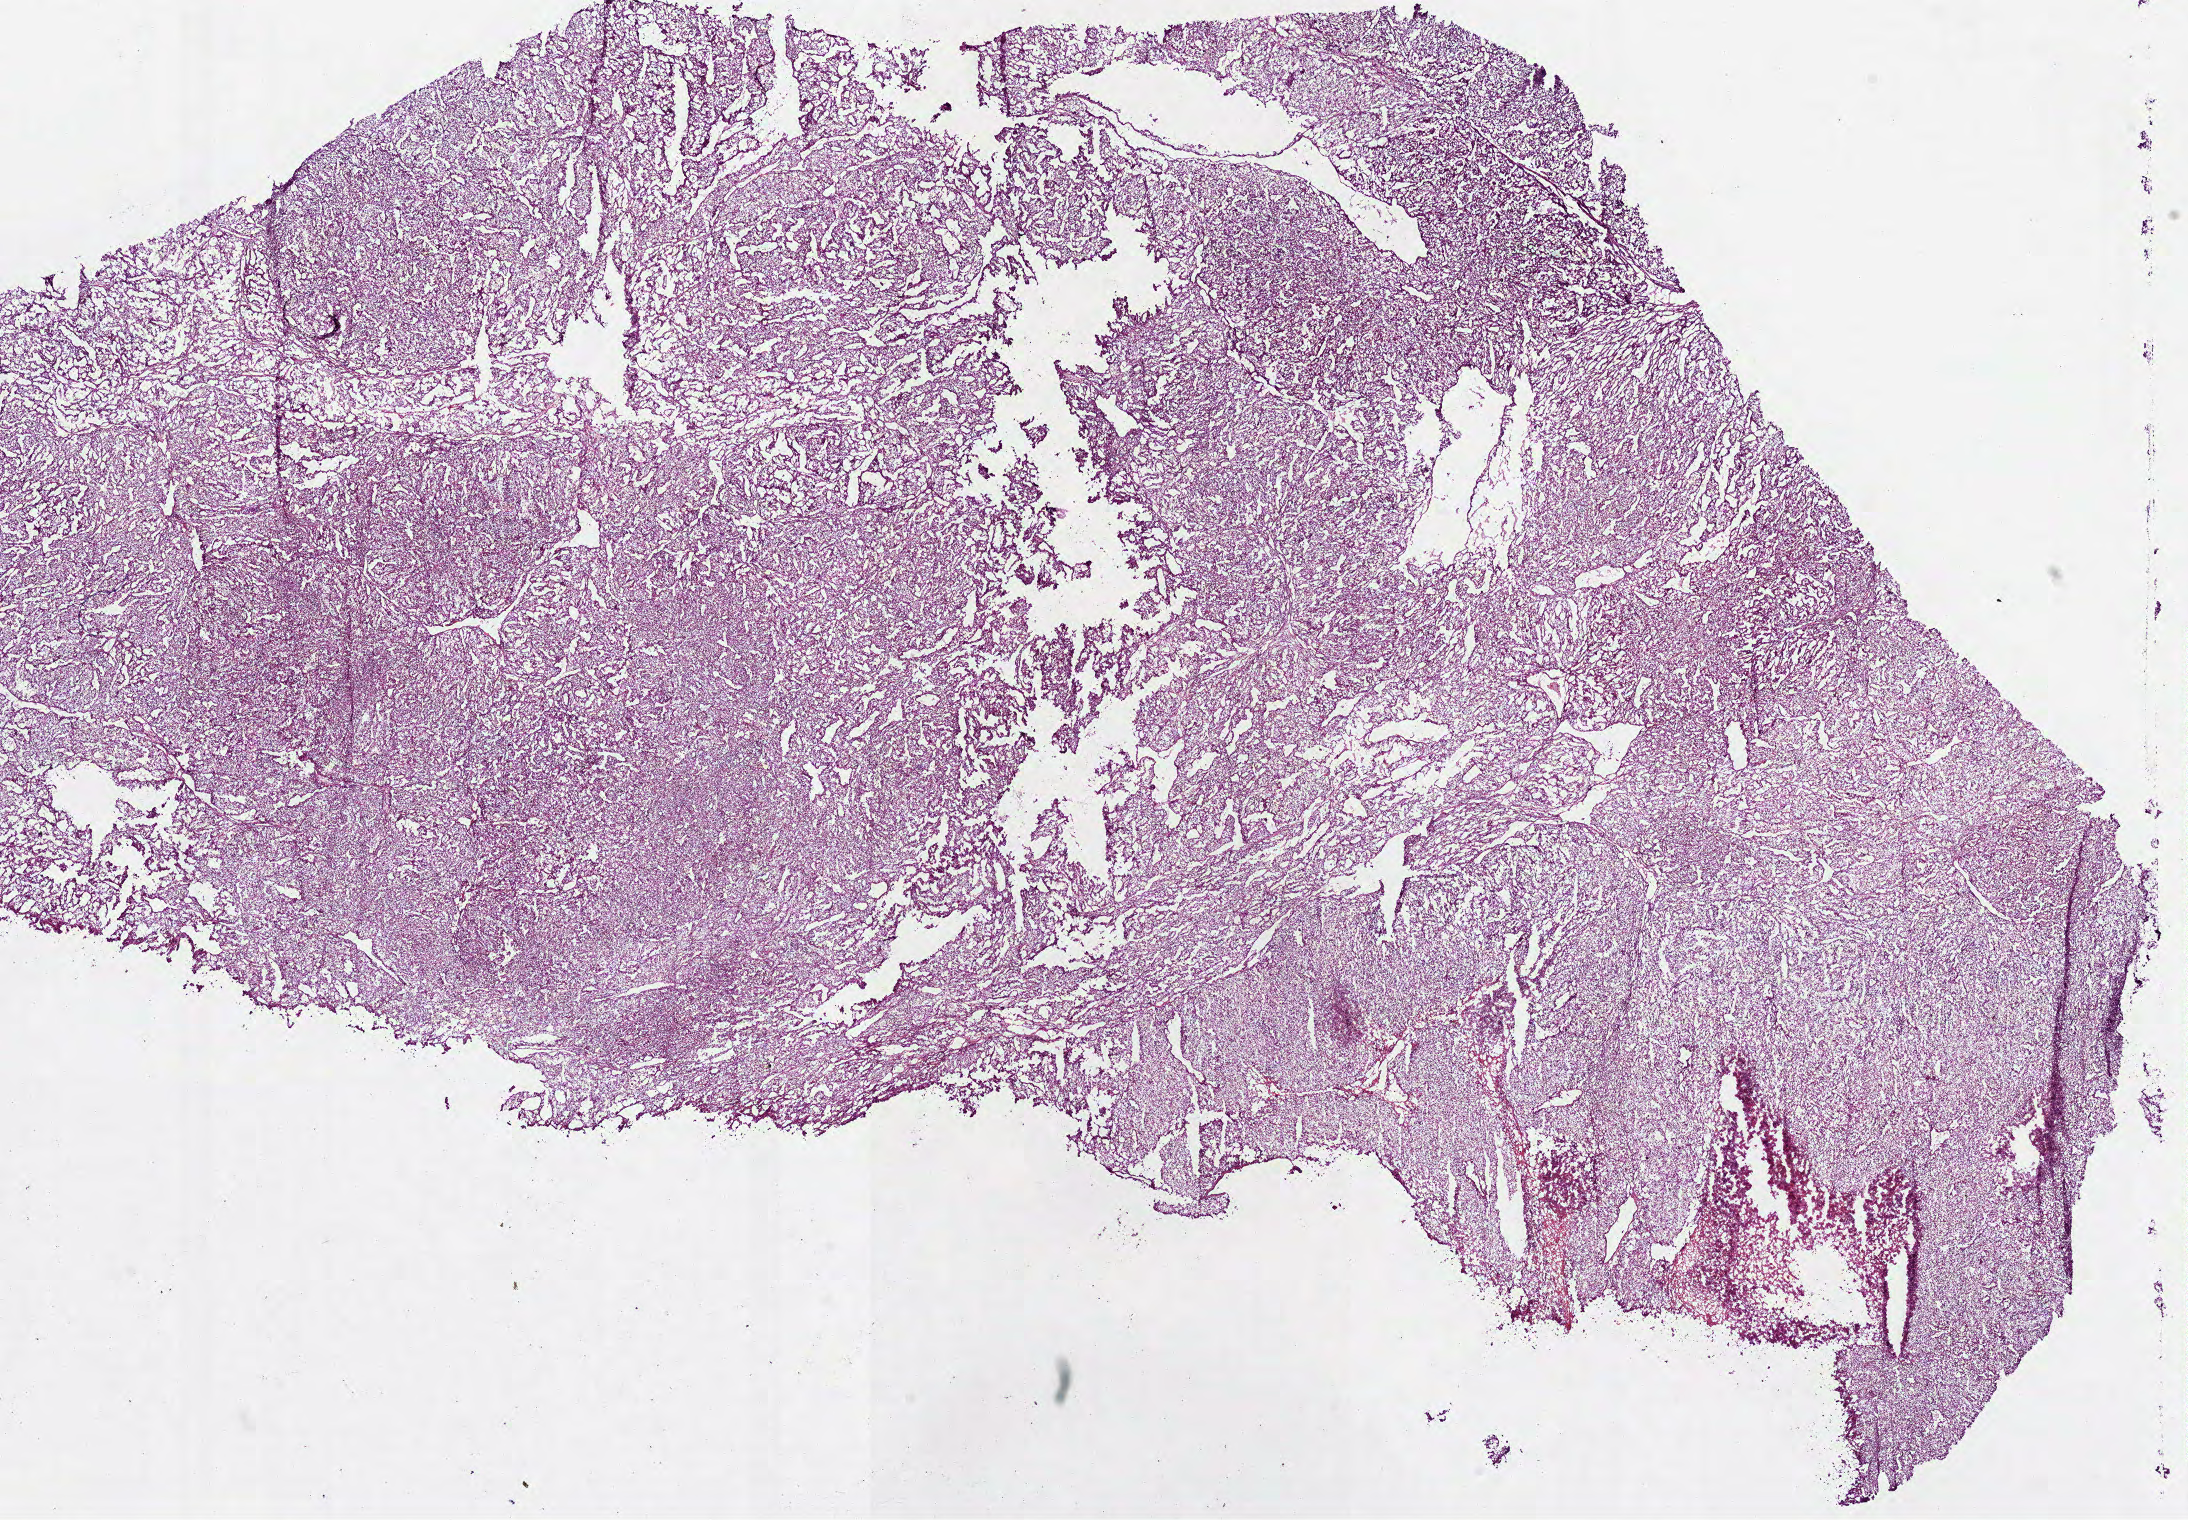
H&E whole-slide image — low-resolution overview of the scanned area, about 17.6 x 12.3 mm; frozen section from the bottom of the tissue portion; kidney, primary tumour sample. Male patient; age at initial diagnosis 60 years. Histologic grade: G2 (moderately differentiated). Slide review estimates, as recorded: tumour cells 93%, tumour nuclei 85%, normal cells 0%, stromal cells 5%, necrosis 2%.
- AJCC pathologic stage: IV (6th edition)
- TNM: T3b NX M1
- pathologic diagnosis: Clear cell adenocarcinoma, NOS